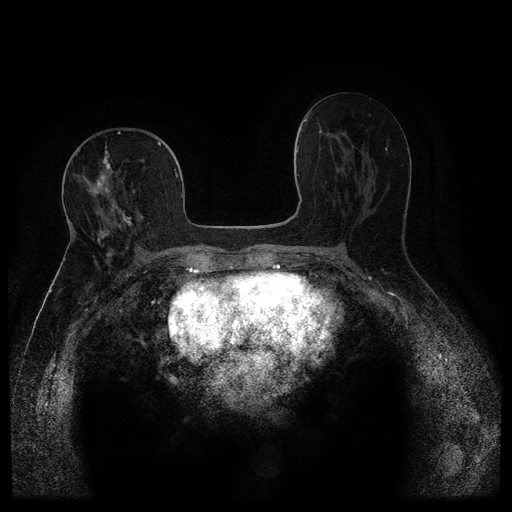
Breast MRI (dynamic contrast-enhanced, multi-phase), one axial slice. Slice 56 of 116 in the series (ordered by position). Dynamic contrast-enhanced series, time point 2 of 5 at this slice position (early post-contrast). 1.5 T. TE 2.6 ms, TR 5.4 ms. 512 × 512 image matrix, field of view 340 × 340 mm. Female patient, age 68 years.
Annotated regions visible in this slice (semi-automatic segmentation, software-assisted and operator-edited):
- breast lesion (labelled 'tumour' in the annotation; benign lesions carry a separate 'benign' label): bounding box (x1, y1, x2, y2) in pixels: (83, 146, 117, 201)